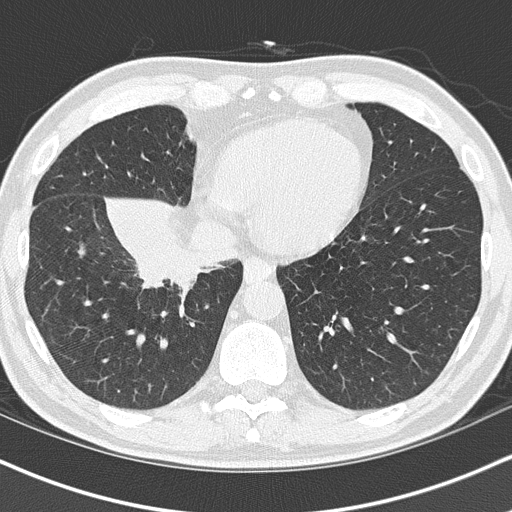
Chest CT (low-dose screening protocol), one axial image. First (baseline) screen. Lung window (W 1500 / L -600 HU). 512 × 512 image matrix. Male participant, aged 55 years at enrolment. Current smoker at enrolment.
- Lesion marked by an expert reader, bounding box <116,221,245,319> (left, top, right, bottom; pixels).
- Screening reader's record for this exam (one nodule recorded; not confirmed to be the boxed lesion): non-calcified nodule or mass ≥4 mm, right lower lobe, 6 × 5 mm, spiculated (stellate) margins, soft tissue attenuation.
- Lung cancer was diagnosed 21 days after this screen: carcinoma, NOS, right hilum, stage IB (AJCC 6th edition), 67 mm at pathology.